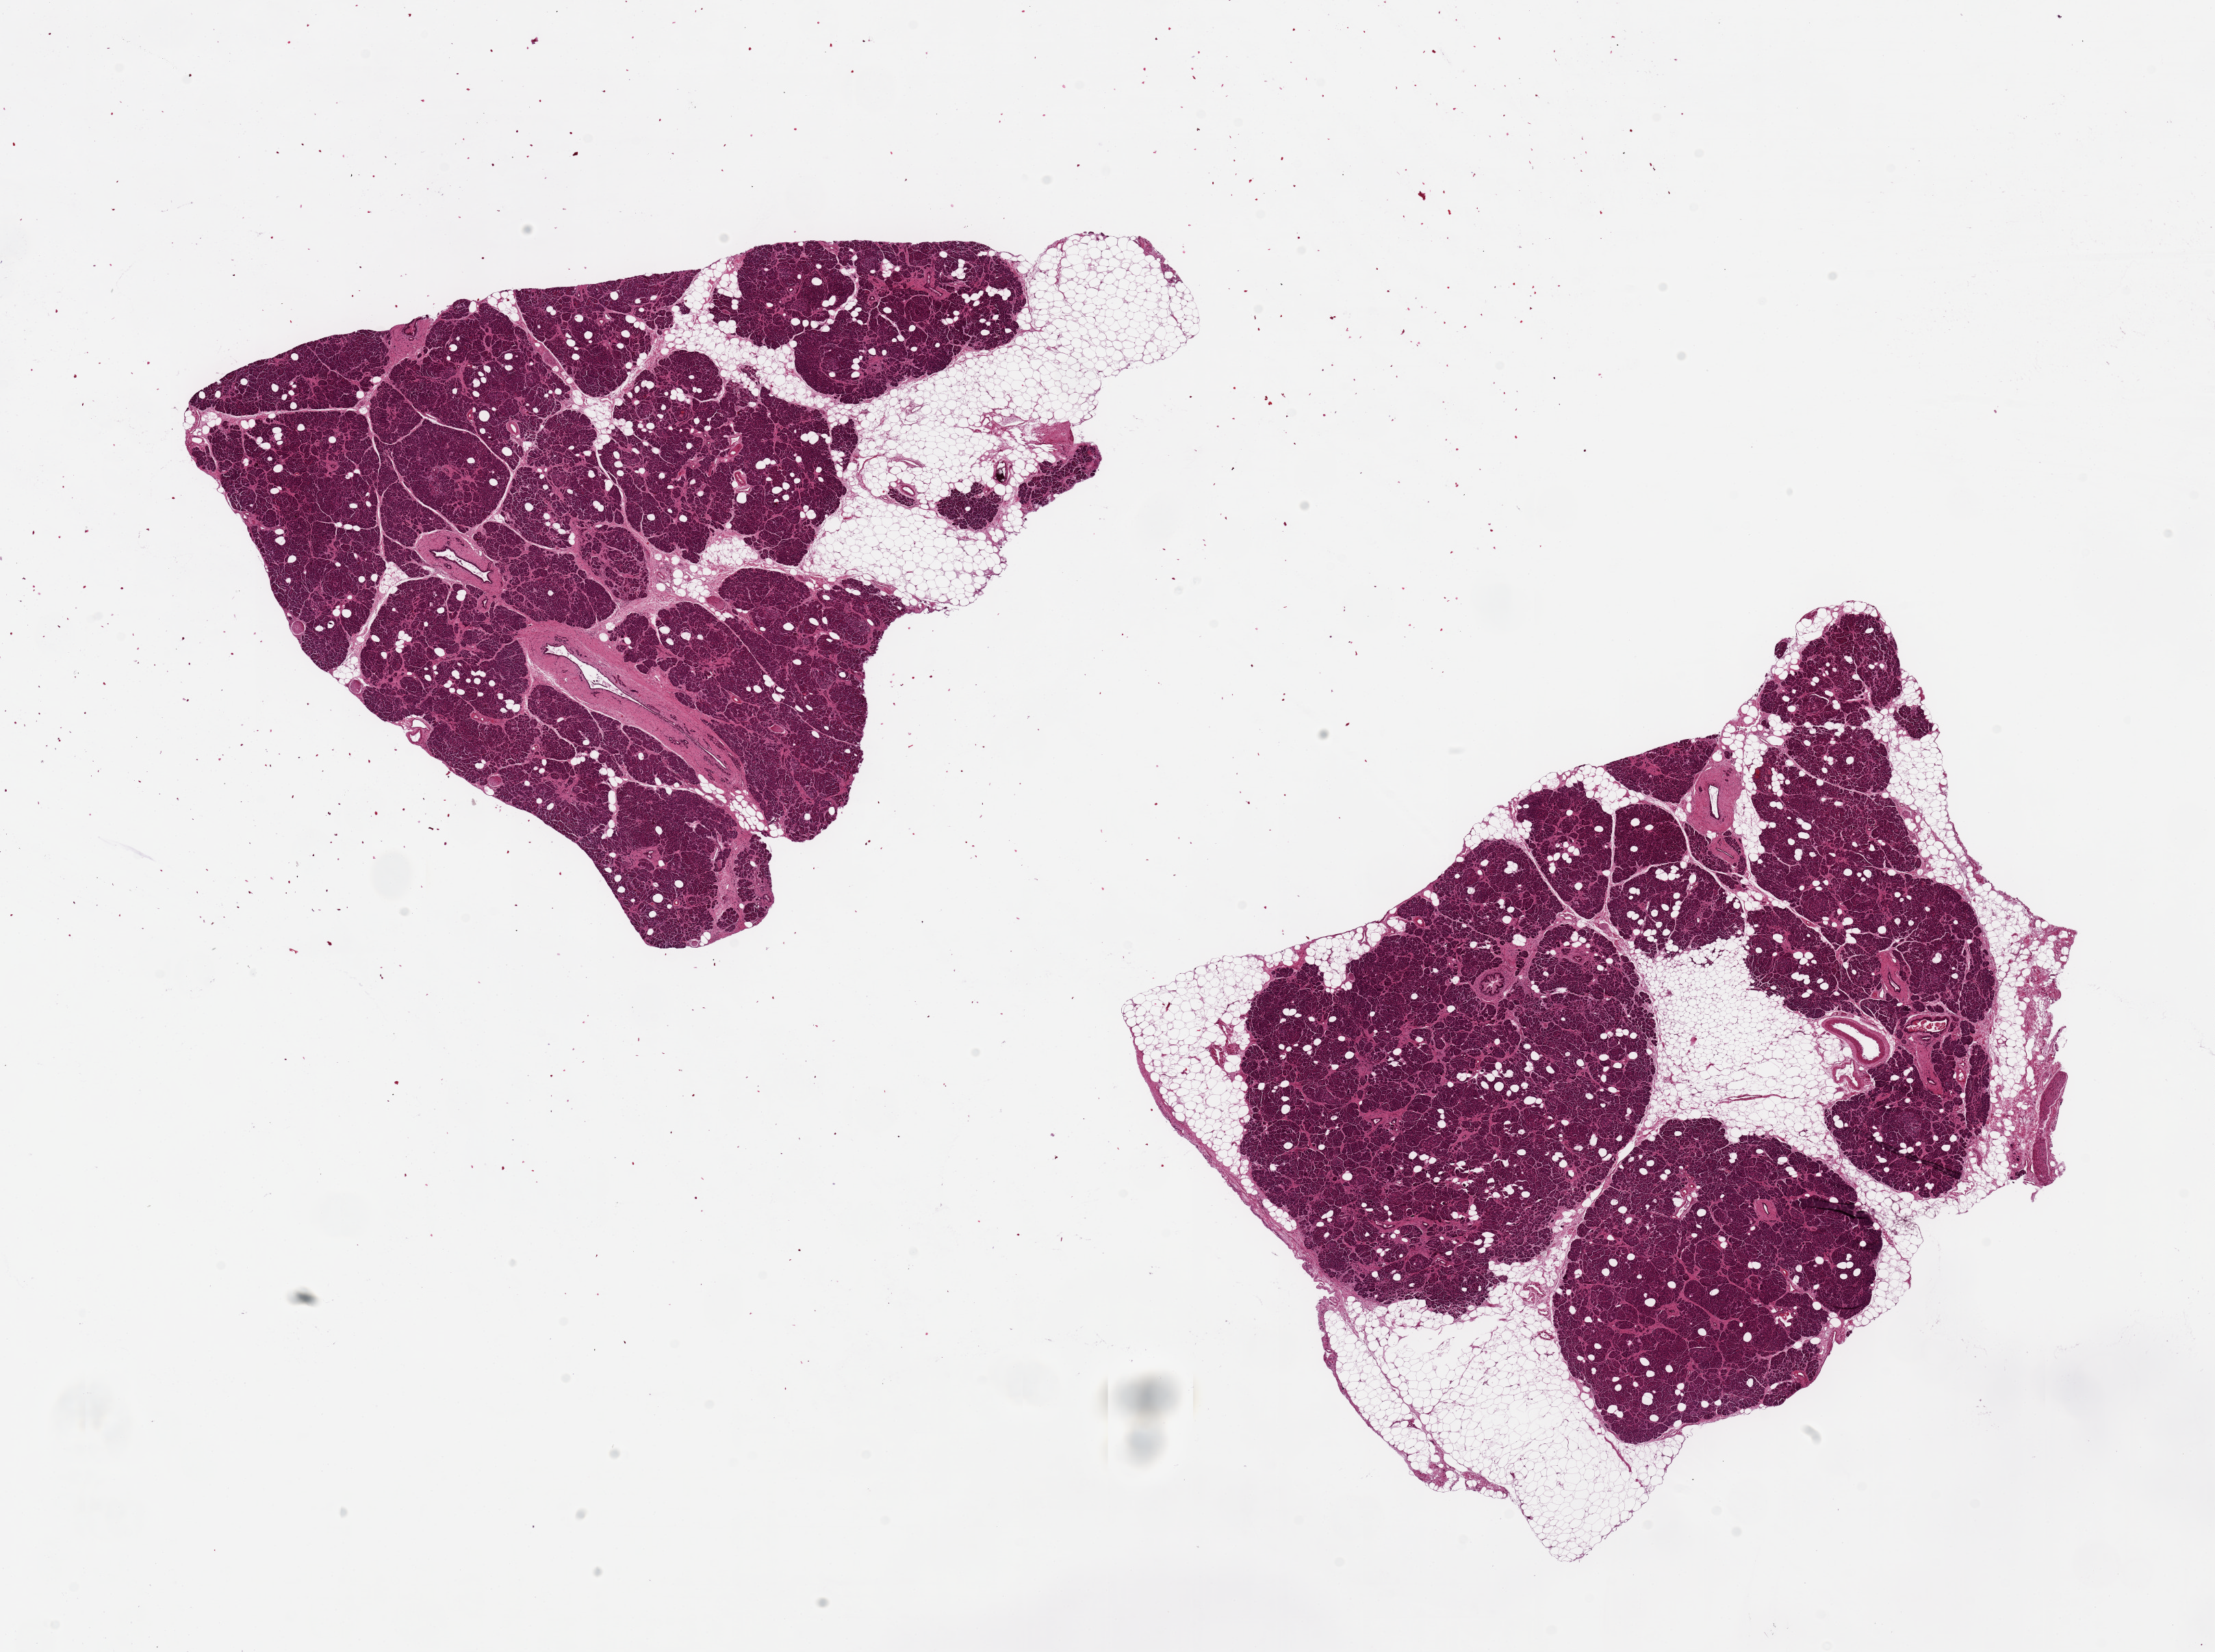
Digitized hematoxylin and eosin (H&E)-stained section — a low-resolution overview of the entire scanned area, about 25.6 x 19.1 mm (slide scanned at 20x); PAXgene-fixed, paraffin-embedded tissue; section of pancreas (target tissue); tissue donor sample. Donor sex: male.
Reviewer comment on this tissue sample: 2 pieces, 11x9 & 10x8mm; well preserved, Islets rare but well seen, adherent fat ~10% of specimen.